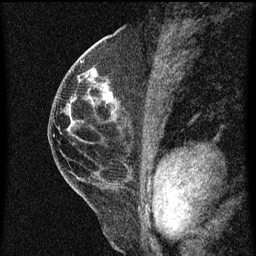
Breast MRI (dynamic contrast-enhanced), one sagittal slice; slice 32 of 60 in the series (ordered by position); dynamic contrast-enhanced series, image 2 of 3 at this slice position (ordered by acquisition); 1.5 T; TE 4.2 ms, TR 8 ms; 2 mm slice thickness; 256 × 256 image matrix, field of view 180 × 180 mm. Patient: female, 48 years.
Annotated regions visible in this slice (semi-automatically segmented with operator editing):
- analysis volume of interest (the breast-tissue region the enhancement analysis was run in; not a lesion): box from (x=89, y=72) to (x=122, y=113) px
- tumour enhancement mask (voxels above the 70 % enhancement threshold inside the analysis volume of interest): (x=101, y=86)–(x=114, y=99)